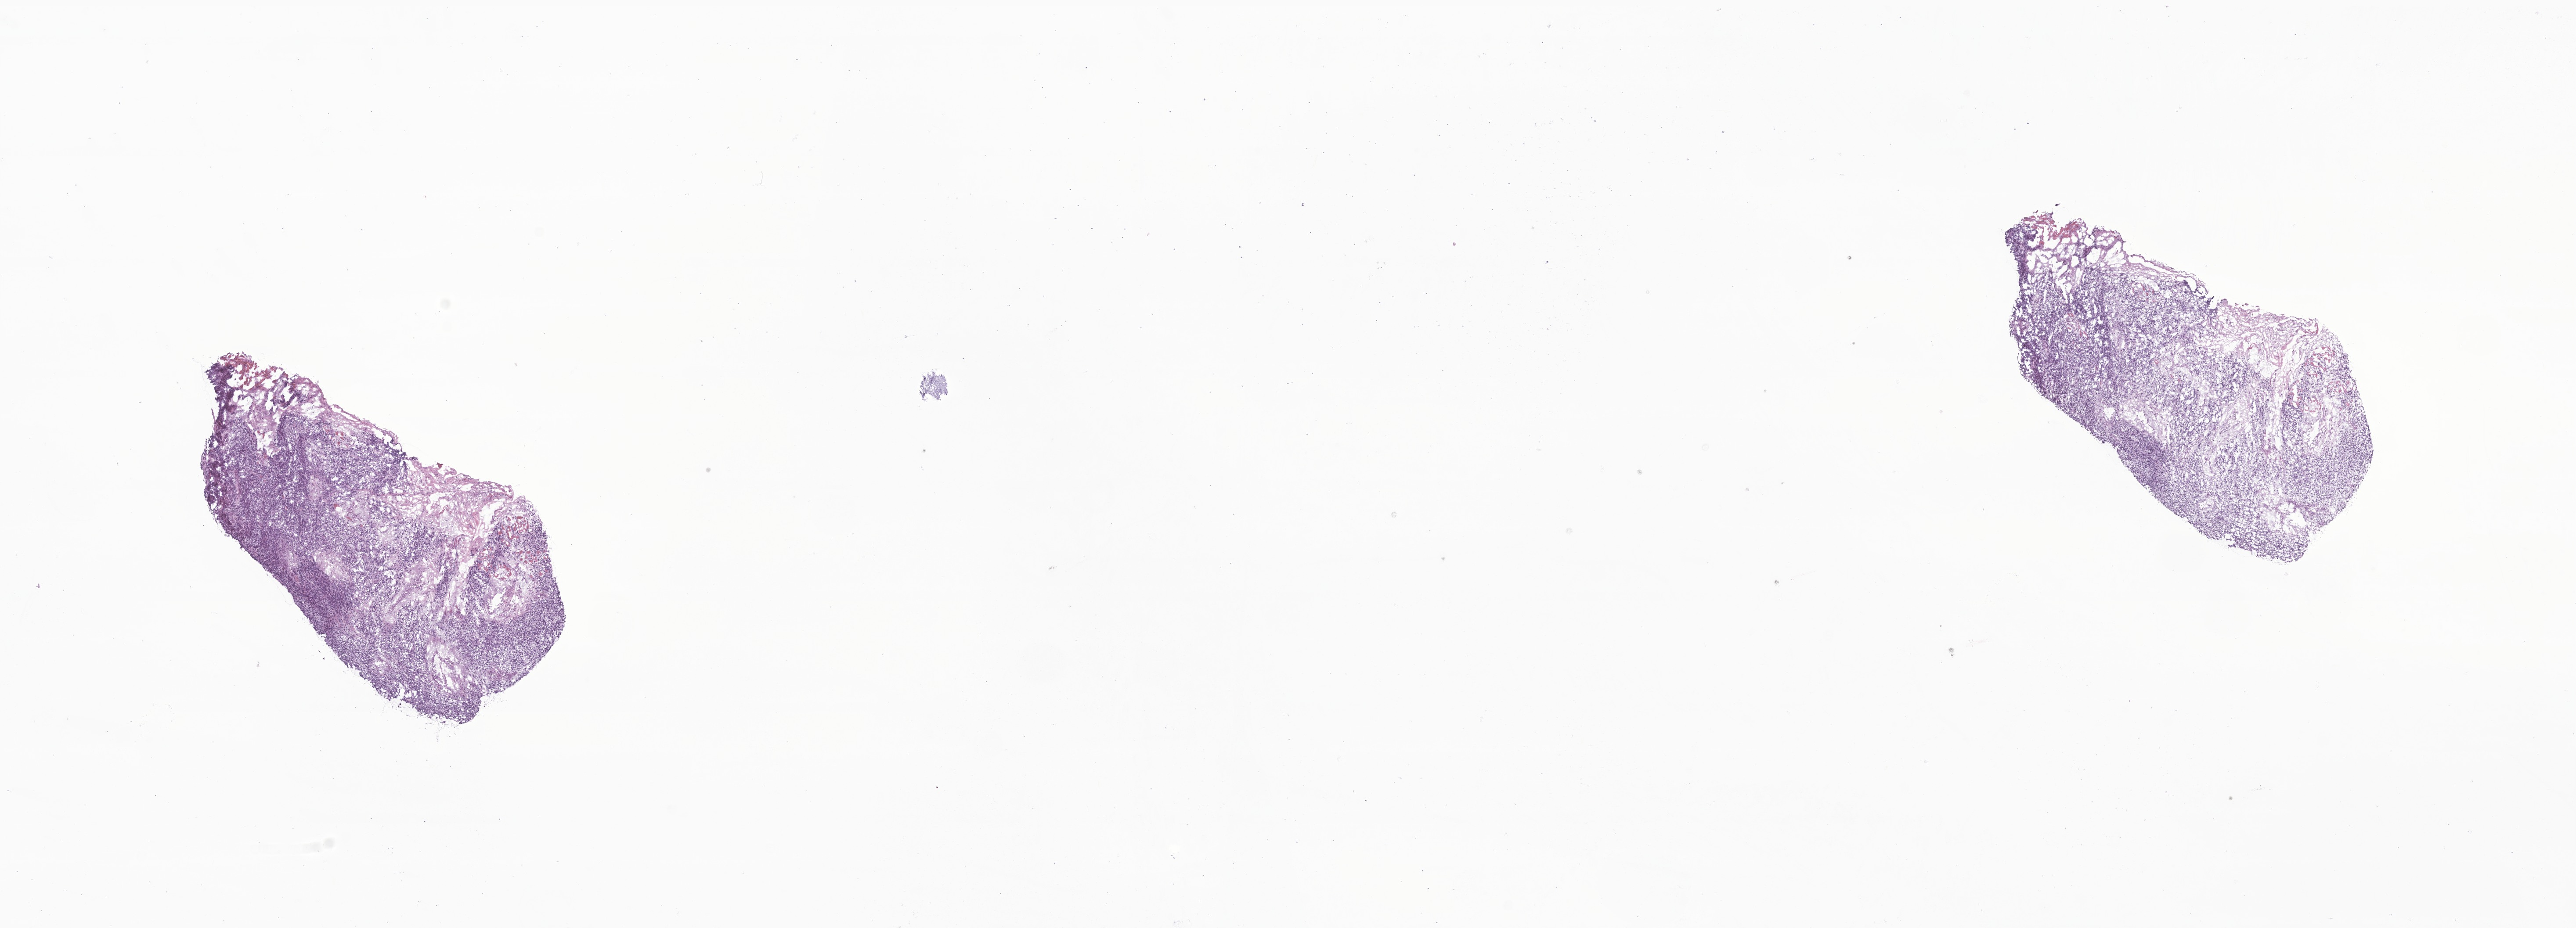
Hematoxylin and eosin (H&E) whole-slide image of tumor tissue from the oropharynx, low-resolution overview of the scanned area, about 24.7 x 8.9 mm. Frozen section (OCT-embedded). Patient female; age 144 months (12 years).
Recorded diagnosis: Rhabdomyosarcoma, NOS.